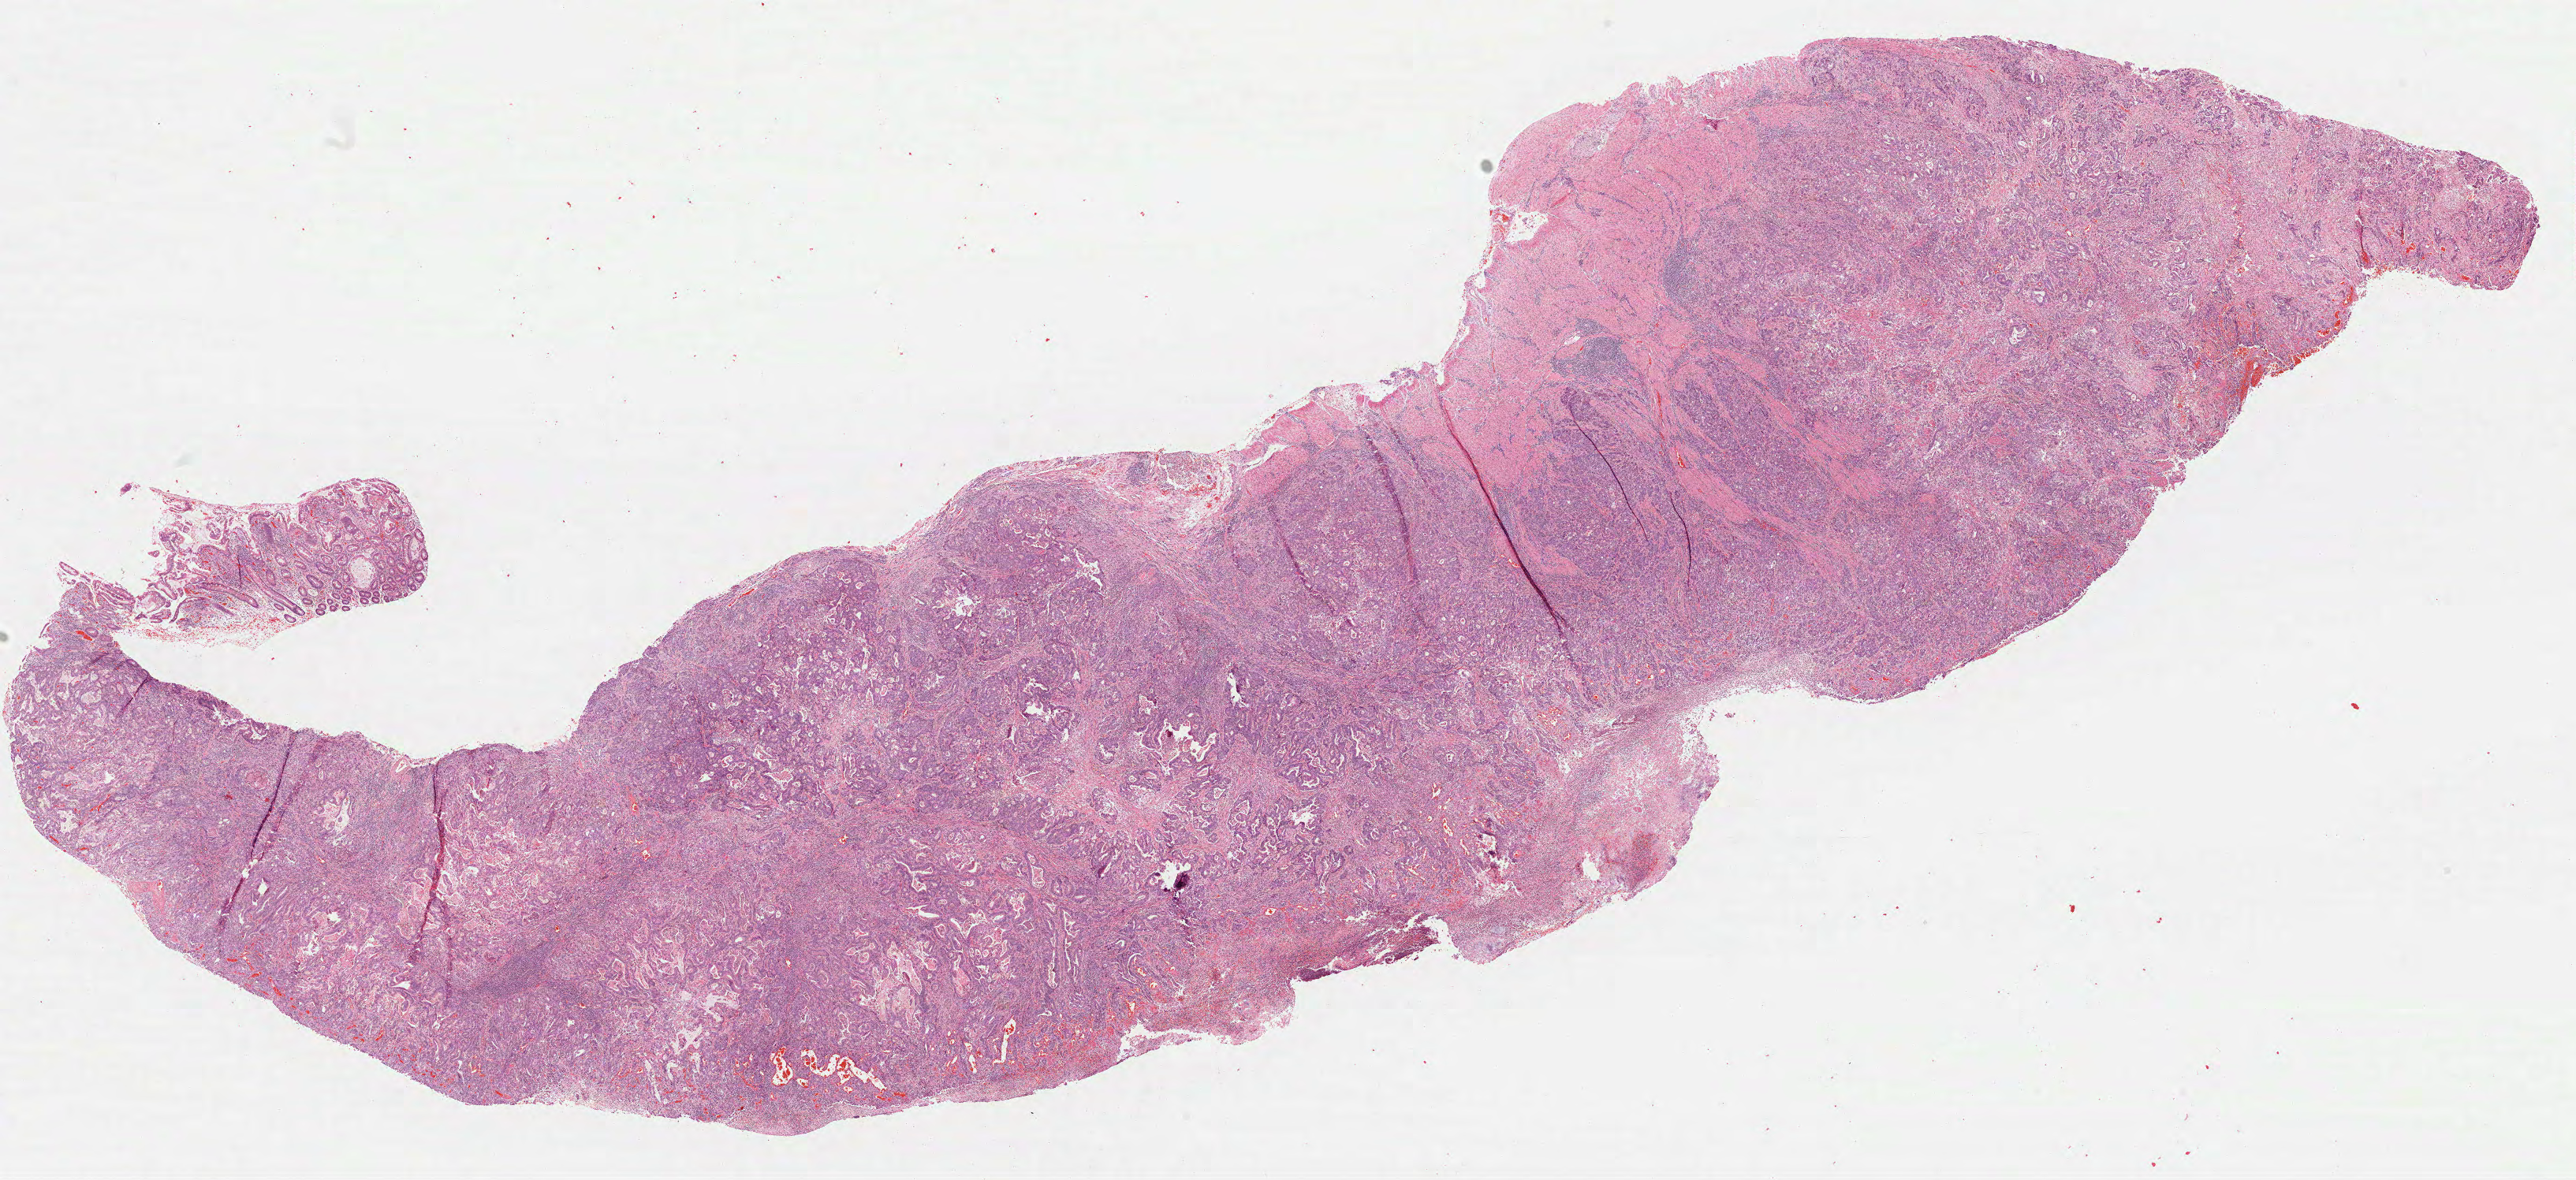
Hematoxylin and eosin (H&E) stained whole-slide image — whole scanned area (about 26.3 x 12.1 mm) shown as a low-resolution overview, formalin-fixed paraffin-embedded (FFPE) diagnostic section, stomach, primary tumour sample. Patient: male, age at initial diagnosis 79 years. Histologic grade: G3 (poorly differentiated).
- AJCC pathologic stage: IIIC (7th edition)
- lymph nodes positive (case pathology): 14 of 14 examined
- histologic diagnosis: Adenocarcinoma, NOS (gastric antrum)